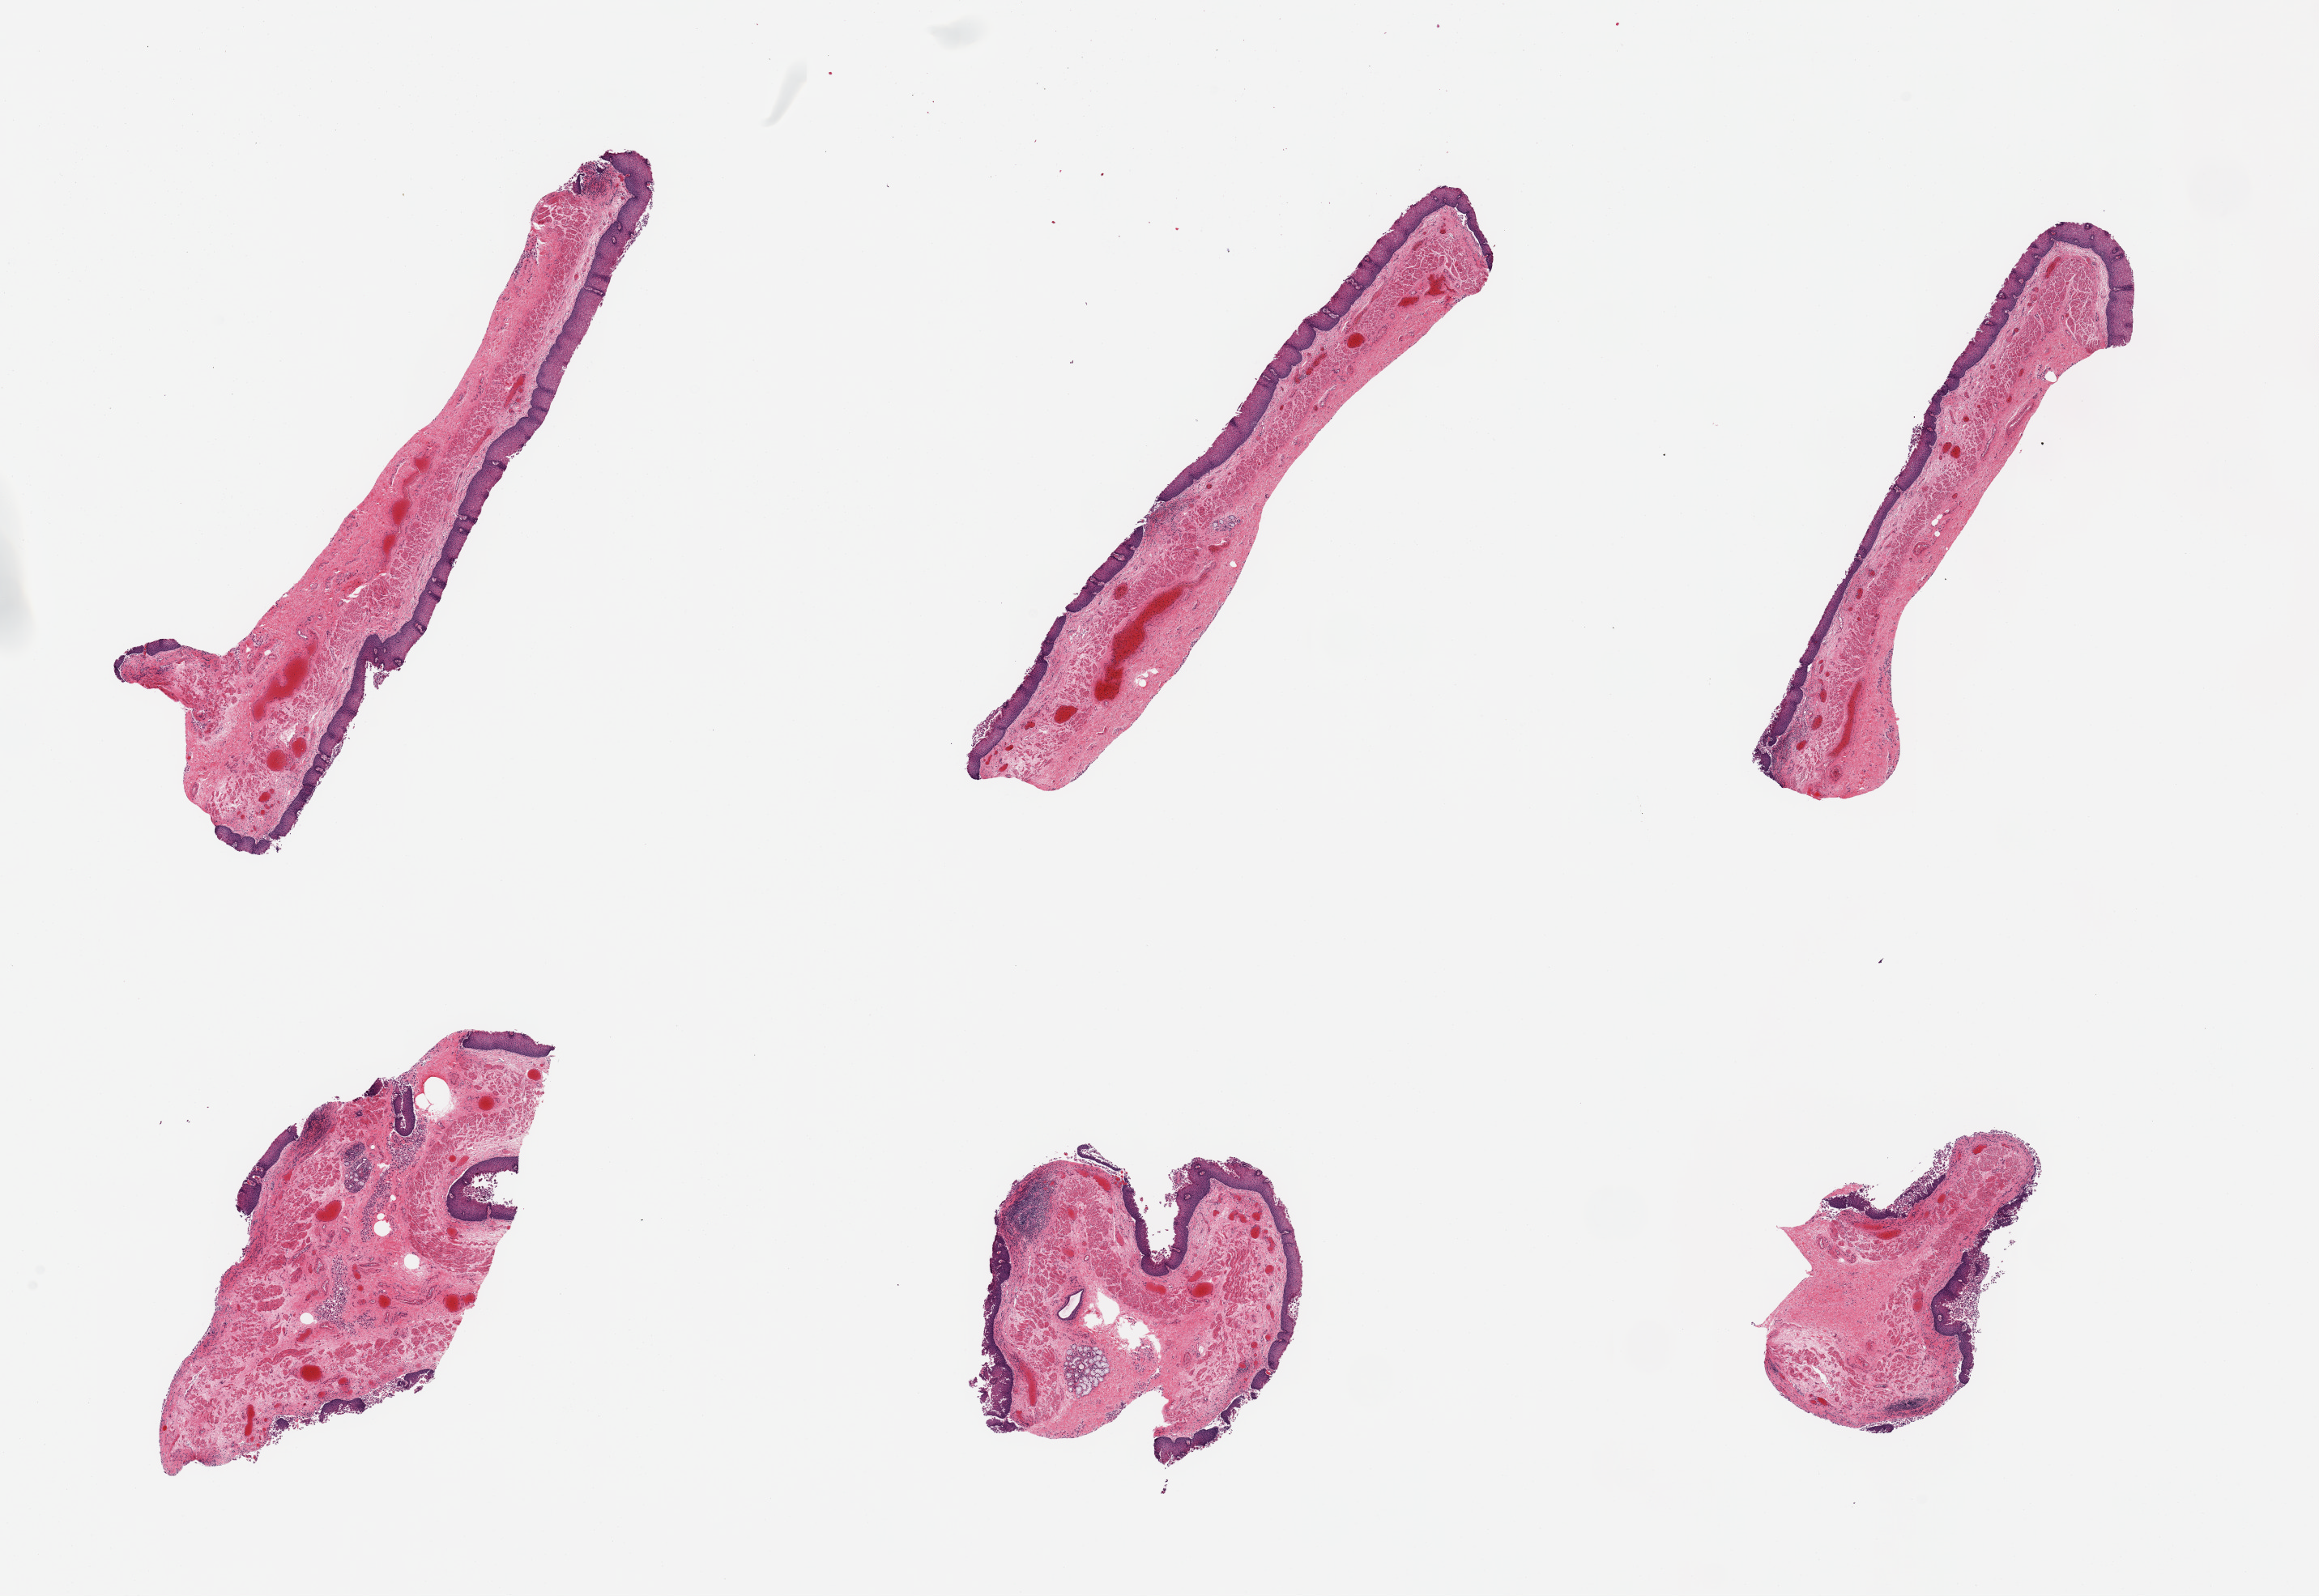
Whole-slide image, hematoxylin and eosin (H&E) stain, brightfield — a low-resolution overview of the entire scanned area, about 22.6 x 15.6 mm; PAXgene-fixed paraffin-embedded (PFPE) section; section of esophageal mucous membrane (target tissue); donor tissue sample. Donor: female.
Reviewer comment on this tissue sample: 6 pieces, target squamous mucosa up to ~0.2mm, ~20-25% thickness, focally sloughing, approaching score 2; Submucosal mucus gland.